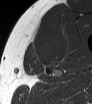
MRI of an extremity soft-tissue mass, one axial slice; slice 41 of 62 in the series (ordered by position); MR volume resampled by the dataset authors to the PET/CT grid (not the native acquisition matrix); 3.27 mm slice thickness; 92 × 104 image matrix, field of view 90 × 102 mm. Male patient. From the clinical record (not read from this slice): histological type: mixoid liposarcoma; grade: low; site of the primary tumour: left thigh.
Annotated regions visible in this slice (expert contour drawn on MRI and transferred to this co-registered scan by the dataset authors):
- gross tumour volume (mass): bounding box [x1, y1, x2, y2] px = [32, 32, 65, 66]